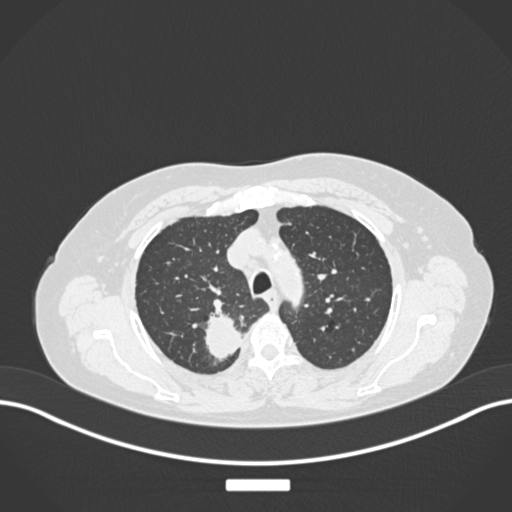
Chest CT, one axial slice. Position 198 of 237 along the scan axis. 120 kVp. Lung window (W 1500 / L -600 HU). 1 mm slice thickness. 512 × 512 image matrix, field of view 400 × 400 mm. Female patient, age 62 years. From the clinical record (not read from this slice): clinical TNM (as recorded): T1c N1 M0.
Outlined on this slice (rectangle marked by the reading radiologist):
- lung tumour (recorded histology: squamous cell carcinoma): bounding box [x1, y1, x2, y2] px = [200, 312, 241, 362]